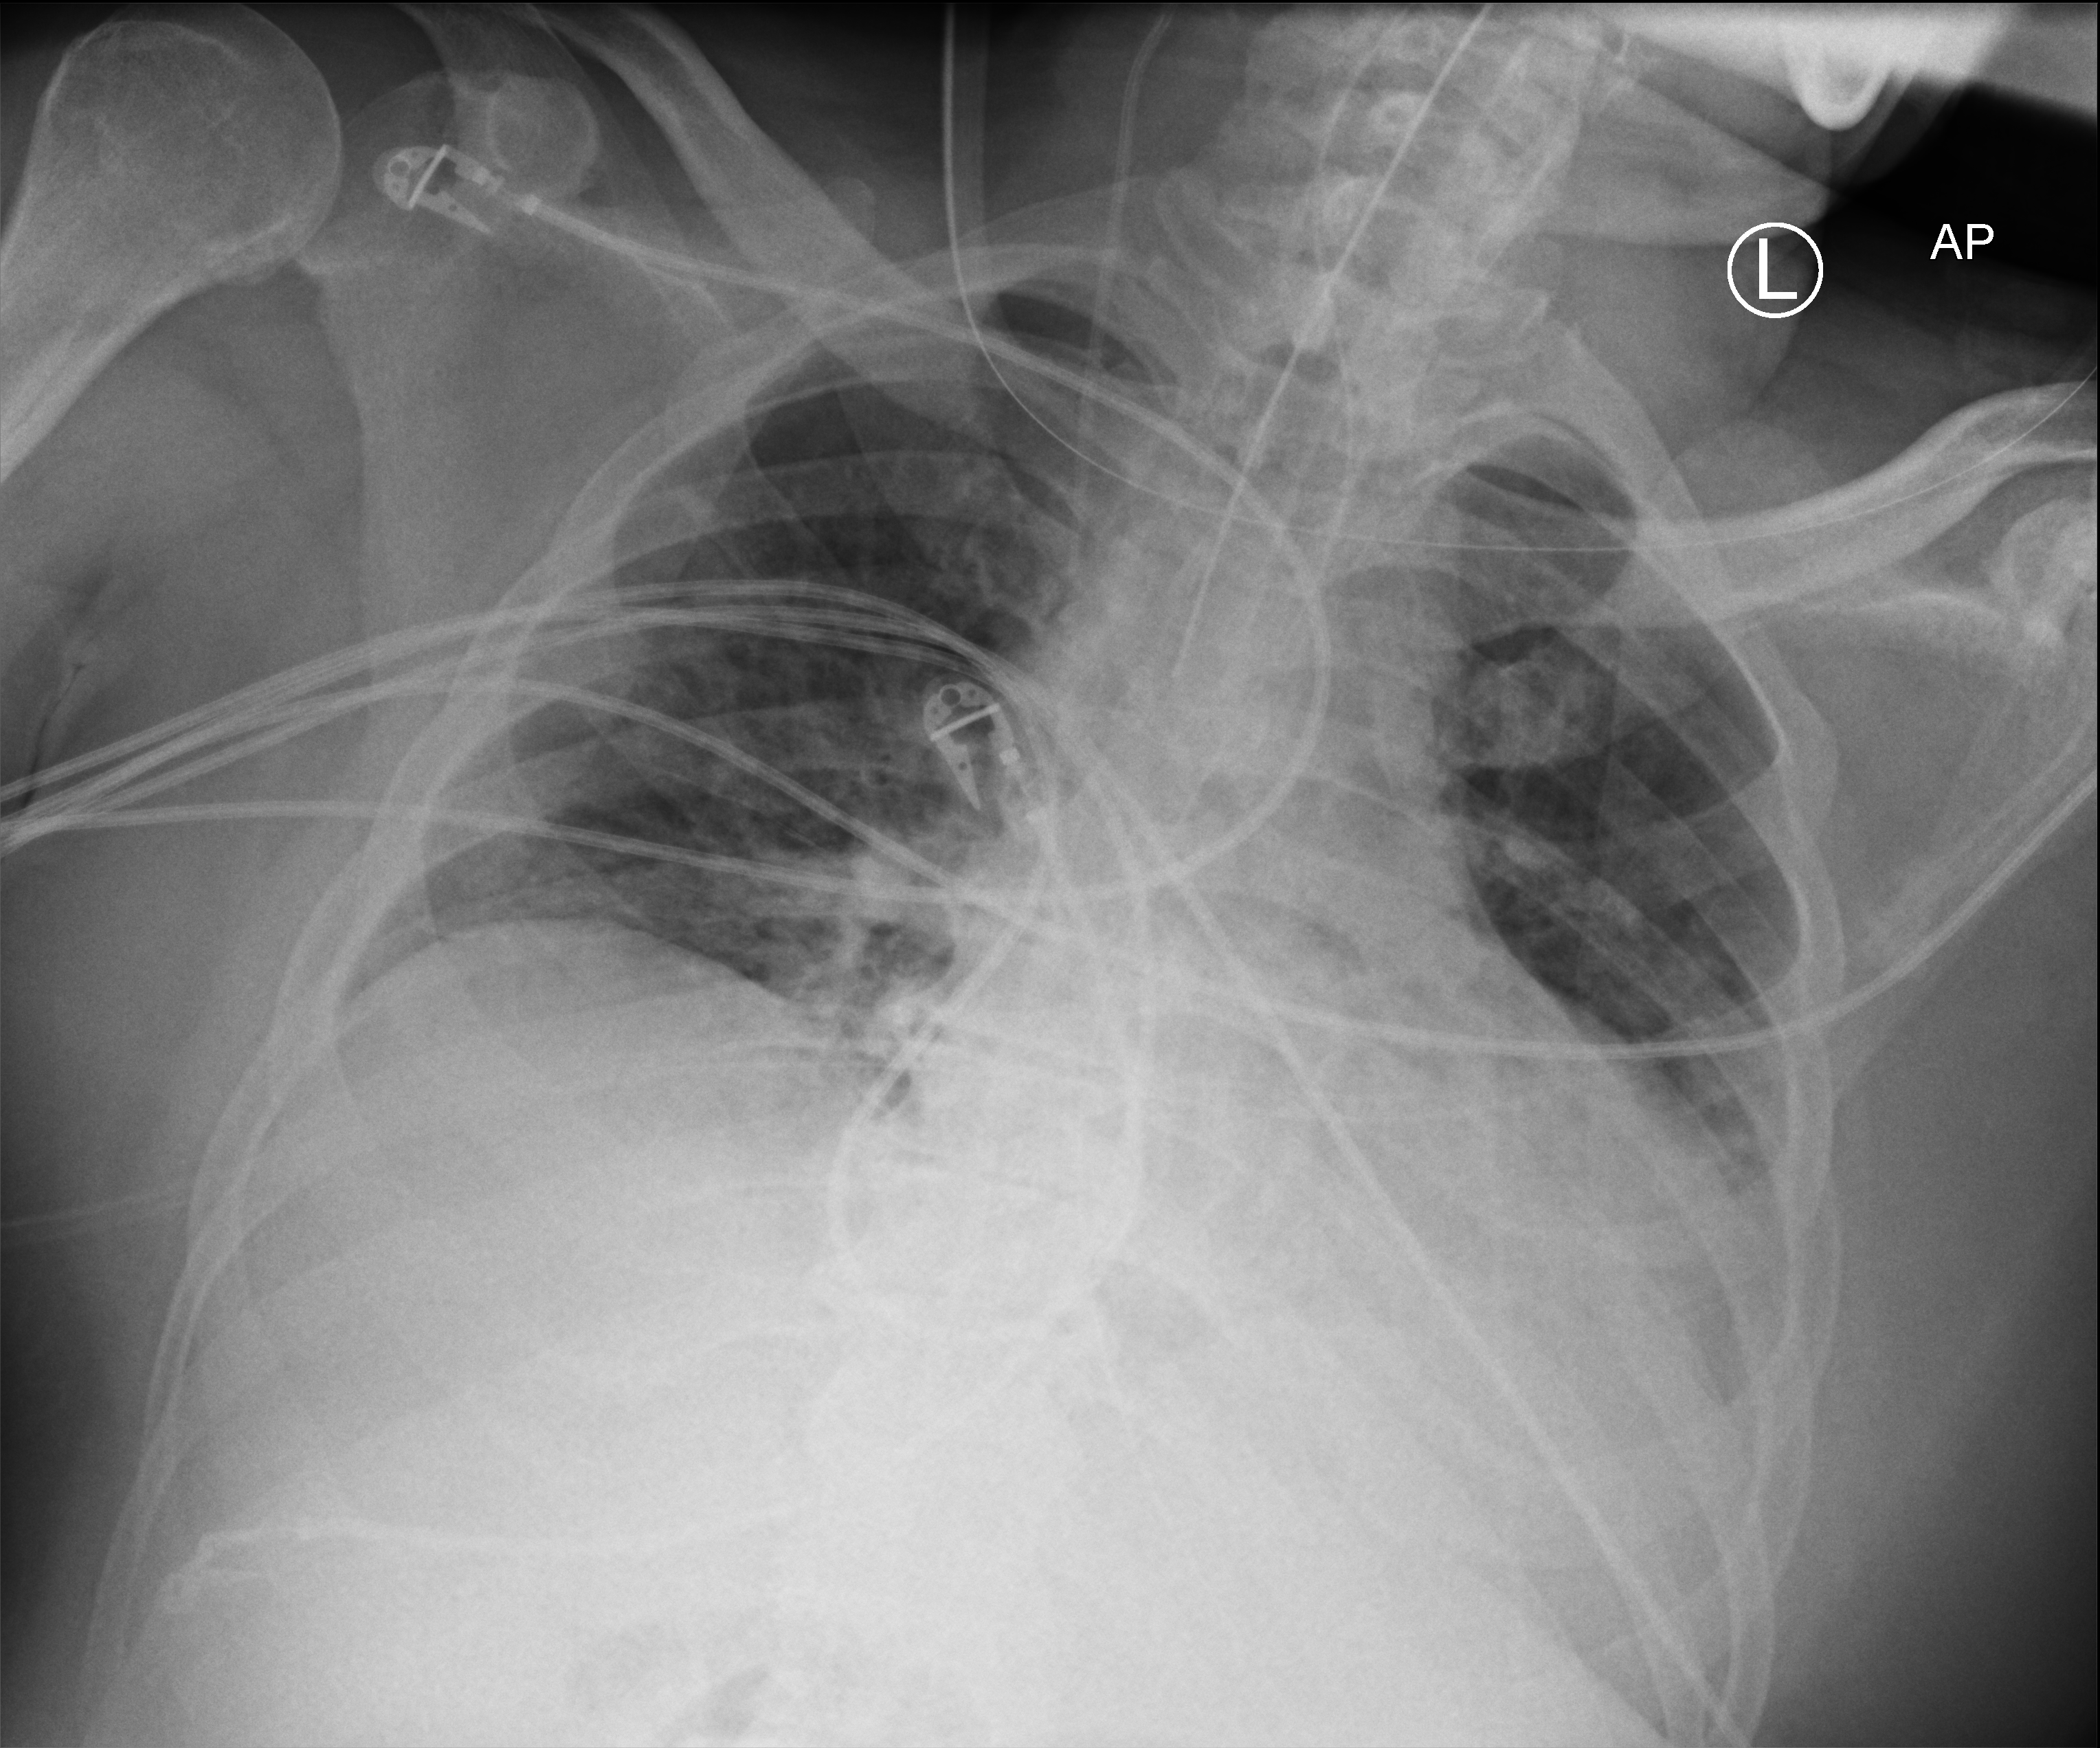
Portable chest radiograph, anteroposterior (AP) projection. Male patient hospitalised with COVID-19, age 18–59 years.
Admission-level facts for this patient (not findings on this image; timing relative to this image not recorded):
- smoking status (admission record): never
- admitted to intensive care during this hospital stay: yes
- mechanically ventilated during this hospital stay: yes